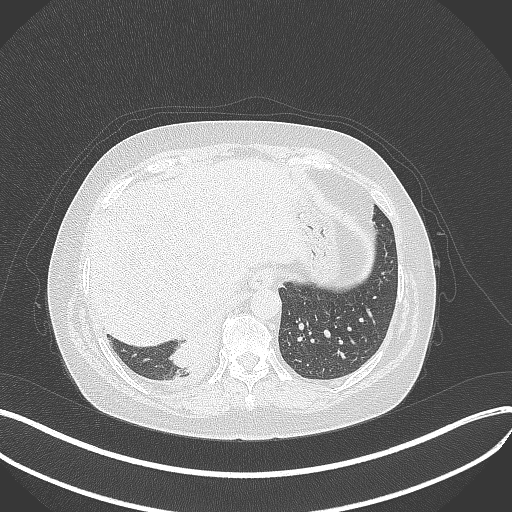
Chest CT, one axial slice; position 81 of 381 along the scan axis; lung window (W 1500 / L -600 HU); 1 mm slice thickness; 512 × 512 image matrix, field of view 400 × 400 mm. Female patient, age 56 years. From the clinical record (not read from this slice): clinical TNM (as recorded): T2b N1 M0; histopathological grade: G3.
Annotated regions visible in this slice (bounding box drawn by a radiologist):
- lung tumour (recorded histology: small cell carcinoma): box from (x=166, y=329) to (x=215, y=371) px